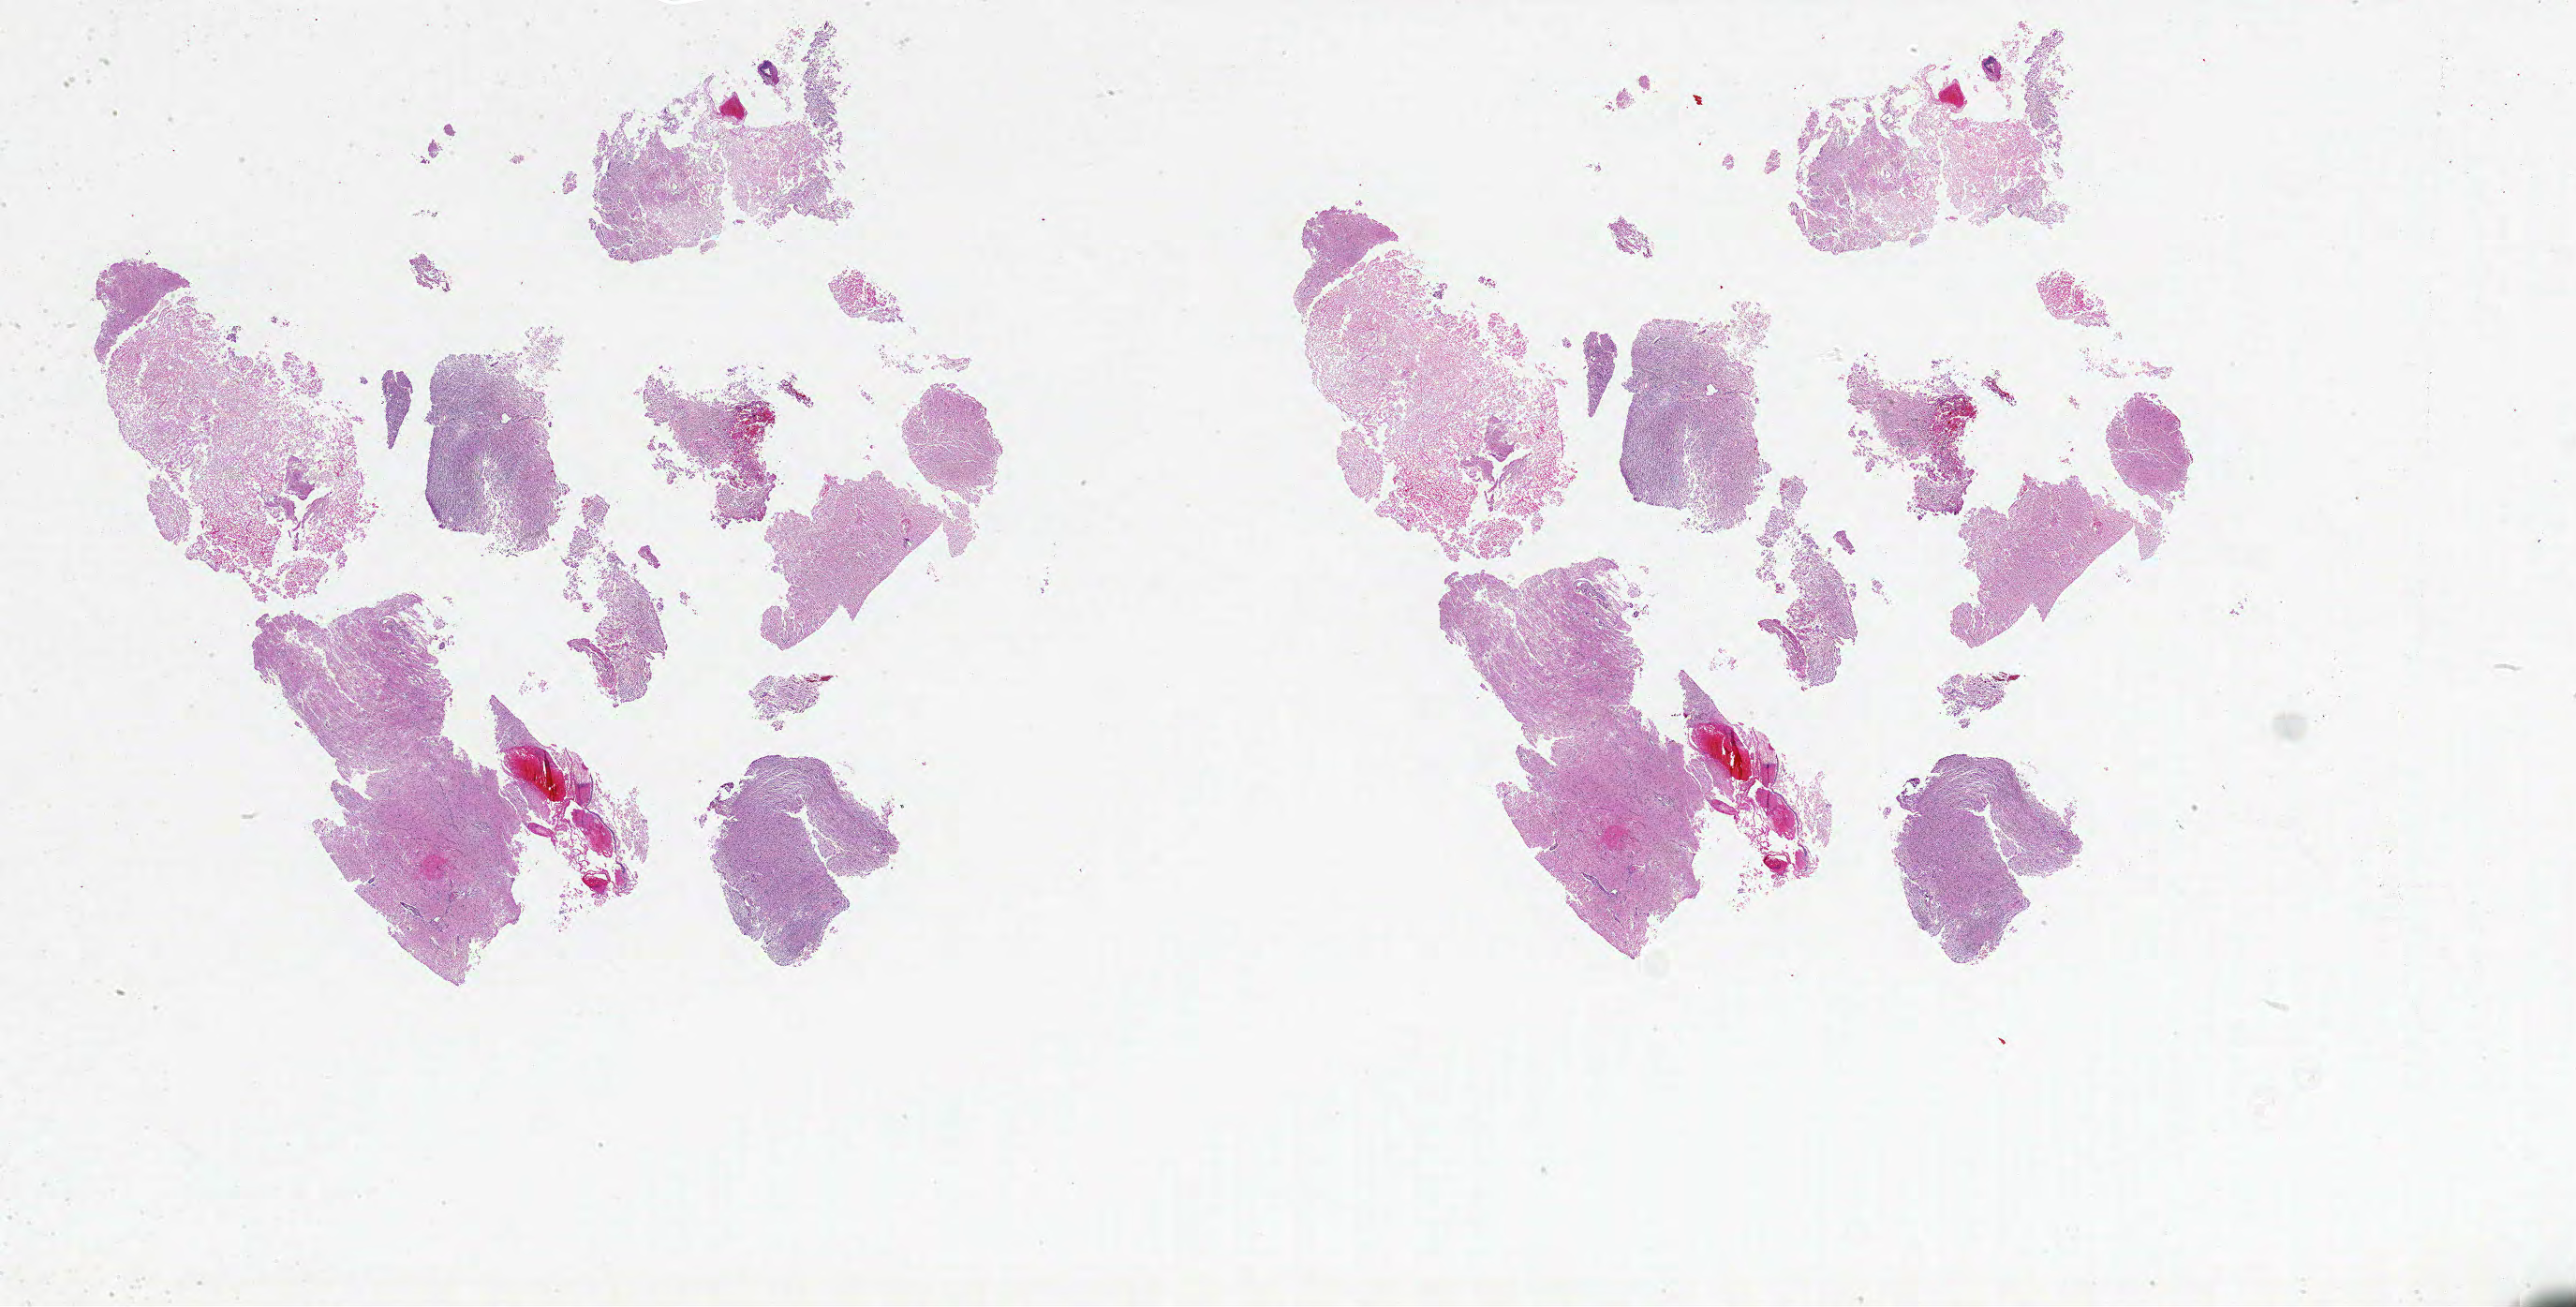
H&E whole-slide image, shown as a low-resolution overview of the whole scanned area (about 44.0 x 22.3 mm); formalin-fixed paraffin-embedded (FFPE) diagnostic section; primary tumour sample from the brain. Patient: male, age at initial diagnosis 56 years.
Histologic diagnosis: Glioblastoma.